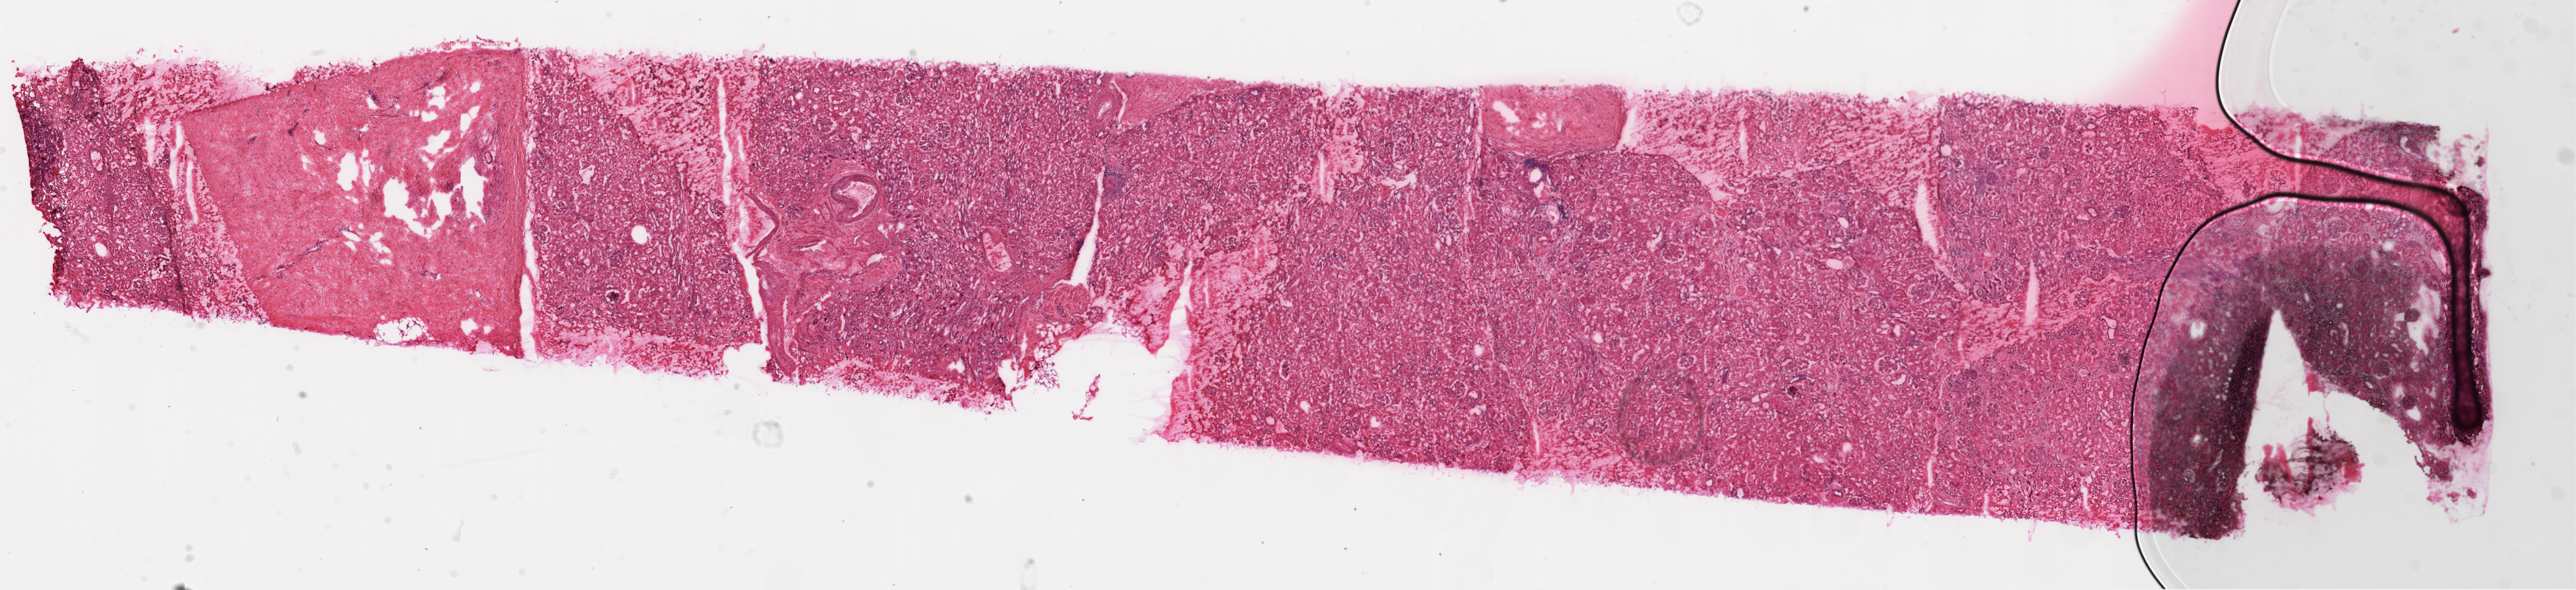
H&E whole-slide image, a low-resolution overview of the entire scanned area, about 28.1 x 6.4 mm (slide scanned at 20x); frozen section; solid tissue normal (non-tumour tissue) sample from the kidney. Female, age 76 years at initial diagnosis.
• this section: solid tissue normal (non-tumour) sample from the same patient
• patient diagnosis: Clear cell adenocarcinoma, NOS